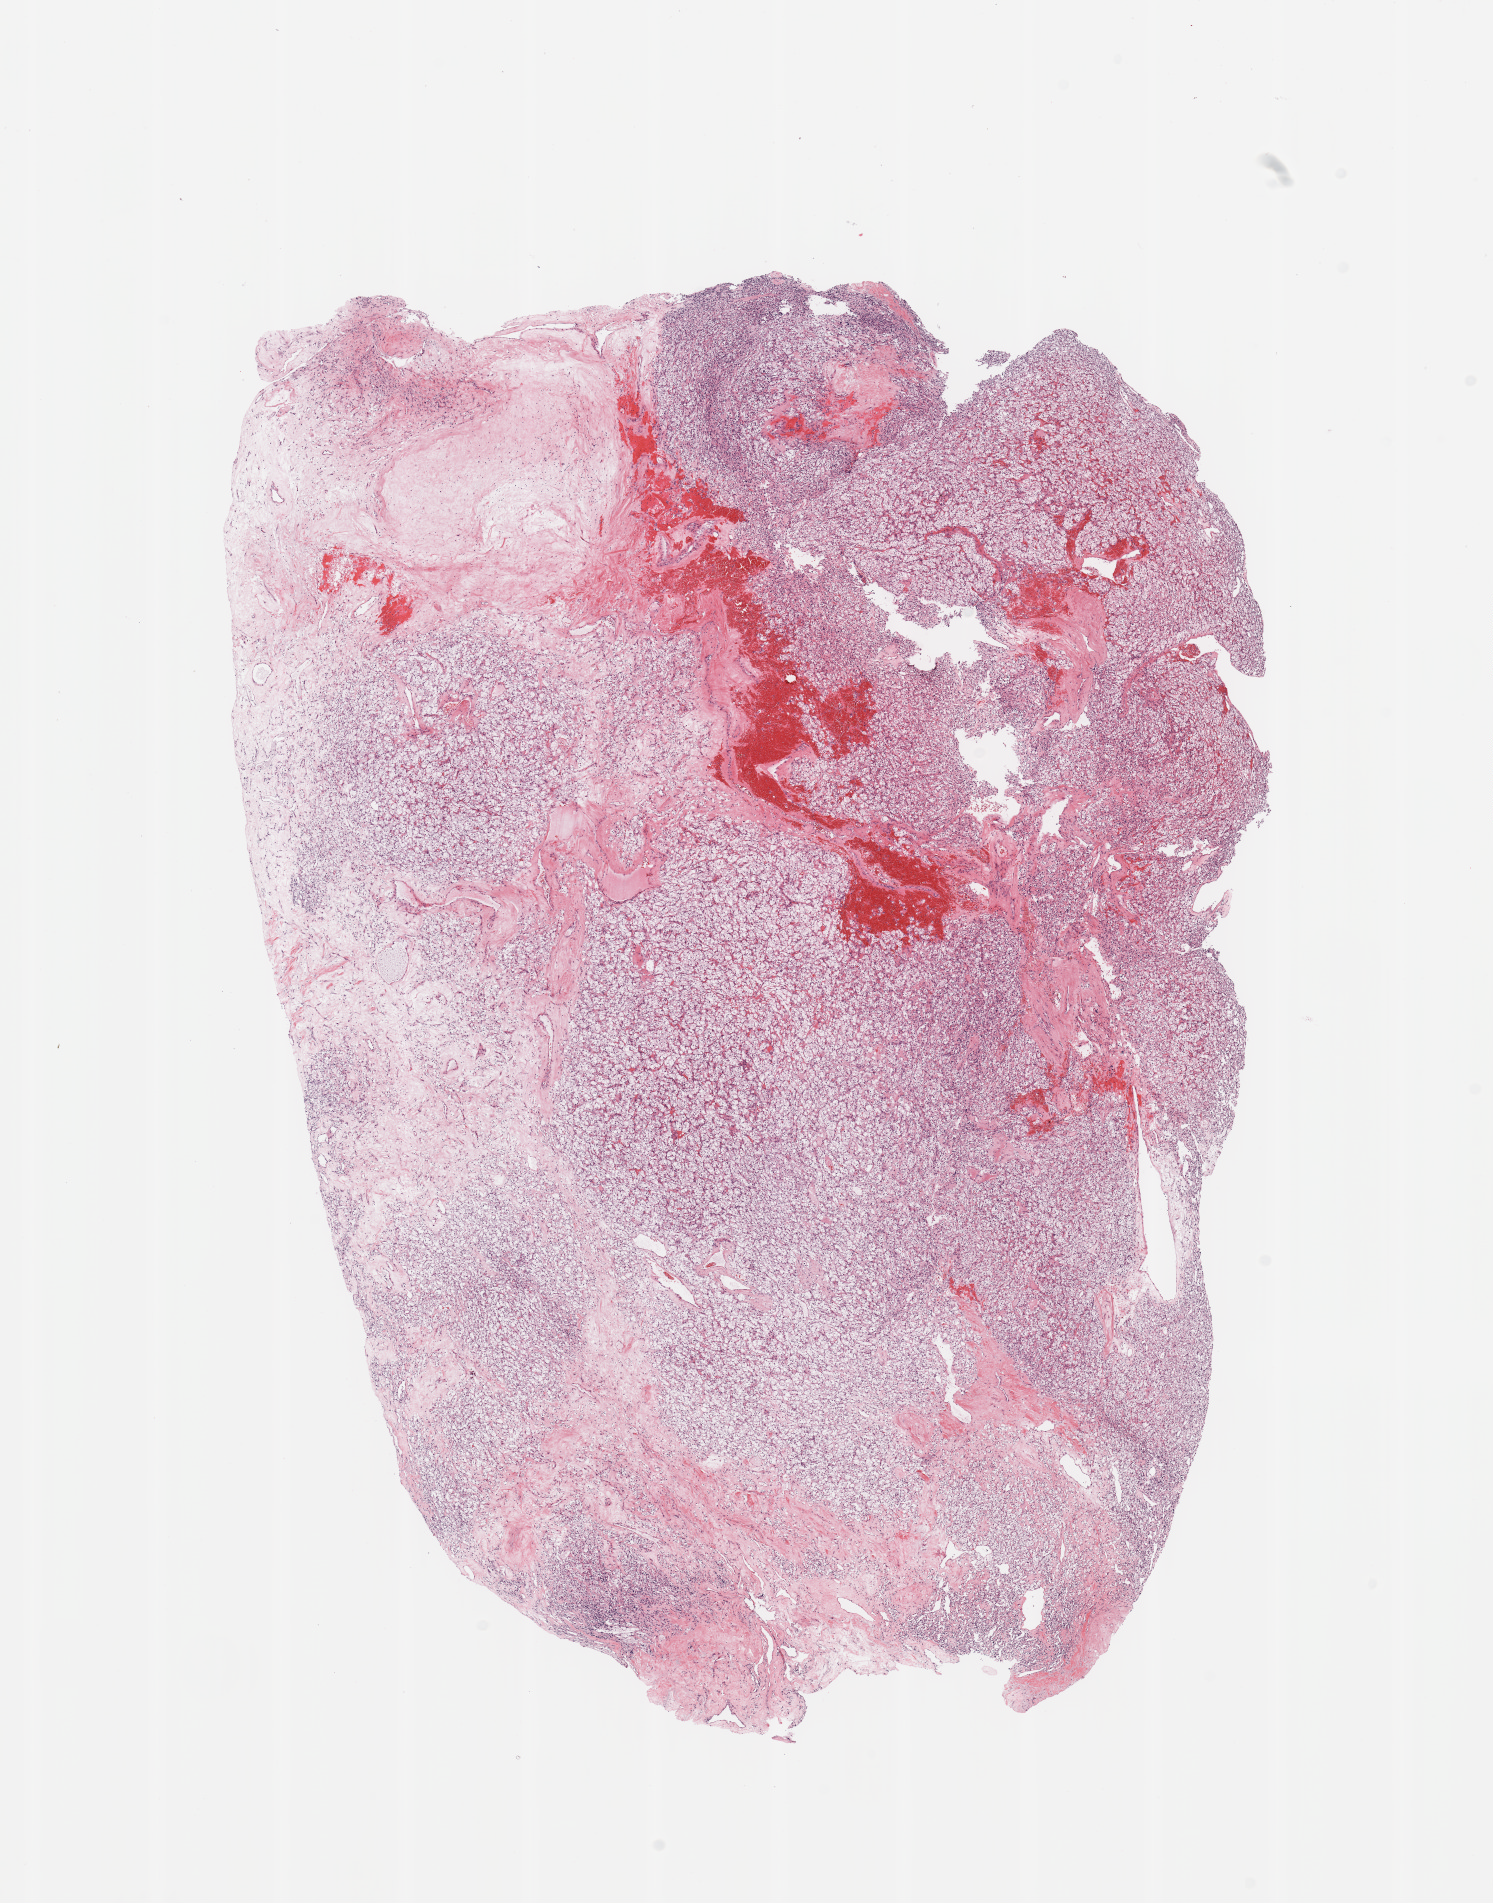
Whole-slide histology image, Hematoxylin and eosin (H&E) stained — a low-resolution overview of the entire scanned area, about 11.8 x 15.1 mm (acquisition: 20x scan); tumour tissue sample, sampled site: kidney. Female, 79 y/o. Histologic grade: G3 (poorly differentiated). Slide review estimates, as recorded: tumour nuclei 85%, necrosis 5%.
- primary tumour site (as recorded): lower pole
- AJCC pathologic stage: I
- histologic diagnosis: Renal cell carcinoma, NOS